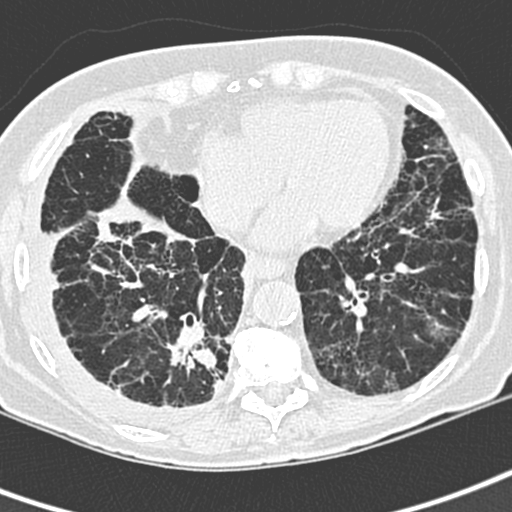
Low-dose screening chest CT, one axial slice. Slice 89 of 220 in the series (ordered by position). 120 kVp. Lung window (W 1500 / L -600 HU). 1.3 mm slice thickness. 512 × 512 image matrix.
Outlined on this slice (manually delineated by an expert):
- lesion 1 (tumor, lower lobe of right lung): bounding box <167,345,216,373> (left, top, right, bottom; pixels)